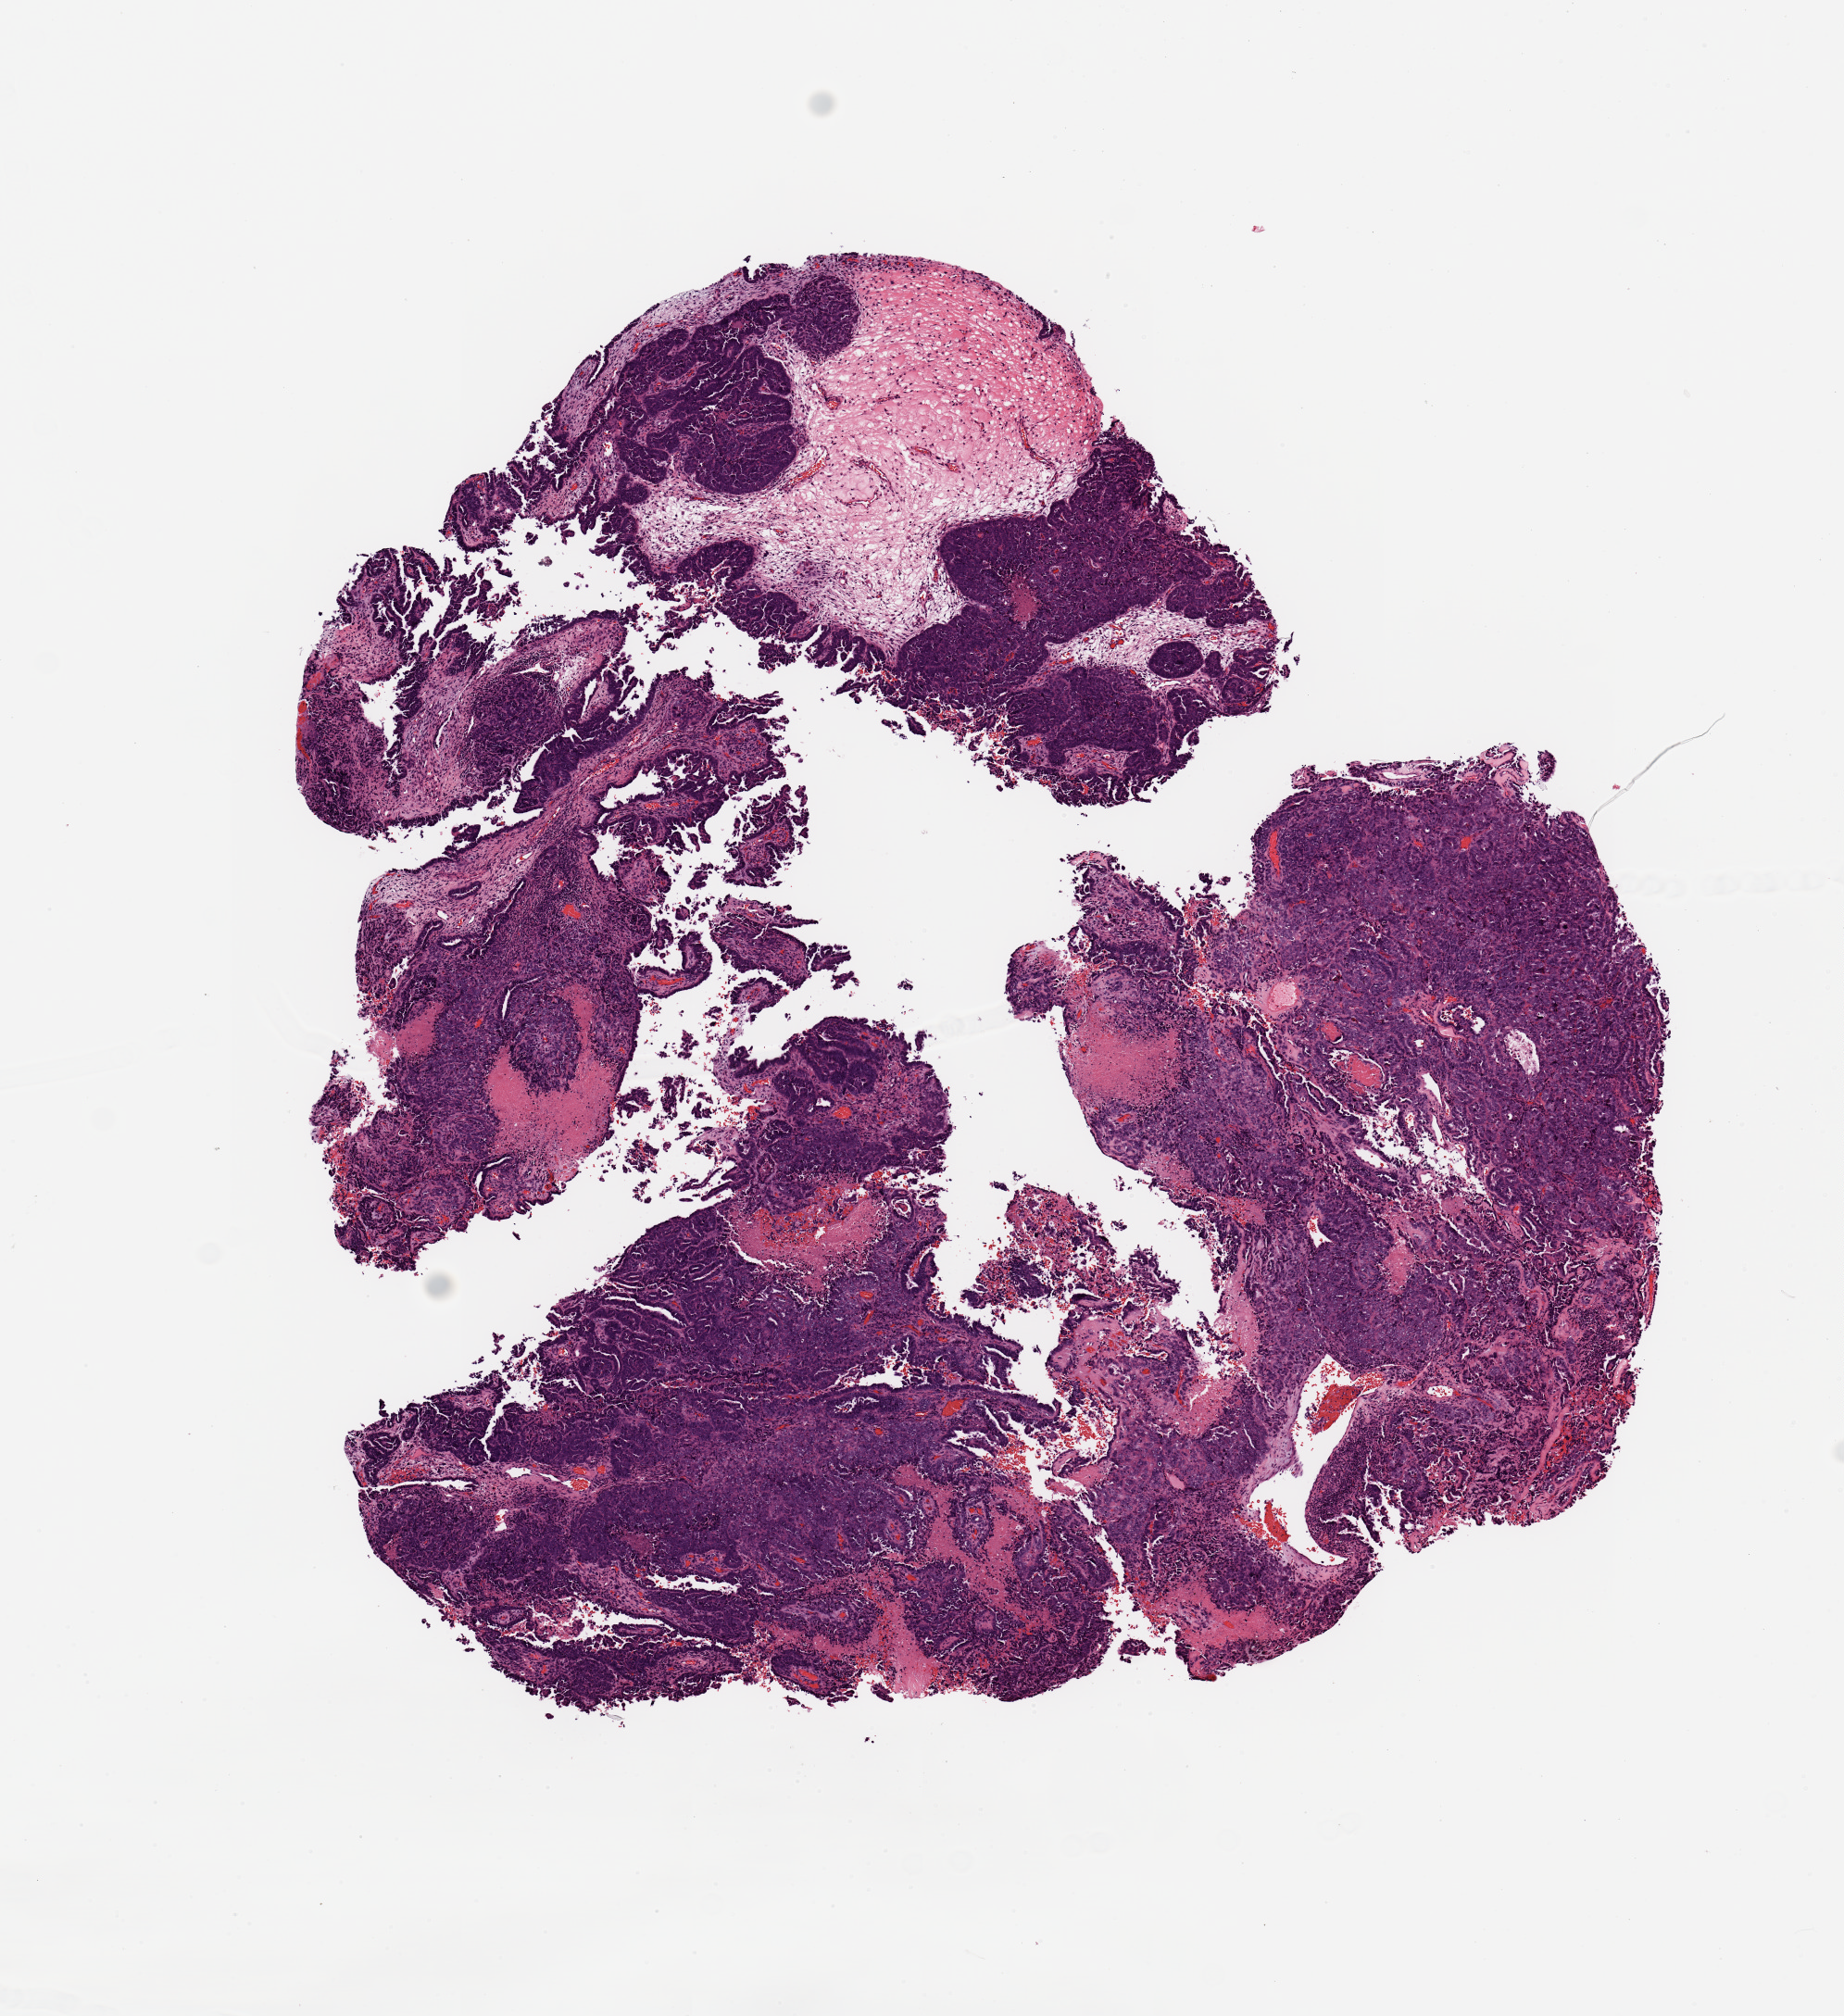
Digitized Hematoxylin and eosin (H&E) stained tissue section (whole slide) — a low-resolution overview of the entire scanned area, about 7.9 x 8.6 mm (slide scanned at 20x). Uterus, tumour tissue. 73-year-old female patient. Histologic grade: G3 (poorly differentiated).
Histologic diagnosis: Endometrioid adenocarcinoma, NOS. AJCC pathologic stage: I.